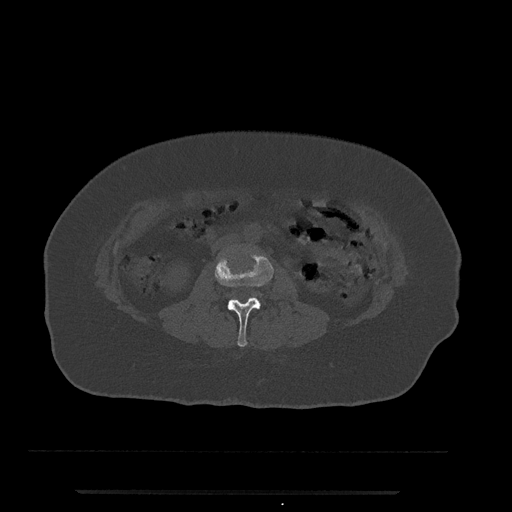
CT including the spine, one axial slice; position 16 of 797 along the scan axis; 120 kVp; bone window (W 1800 / L 400 HU); 0.5 mm slice thickness; 512 × 512 image matrix, field of view 440 × 440 mm. Female patient, age 51 years. Case-level facts recorded for this patient, not image findings: primary cancer: neuro; vertebrae with lytic lesions (as recorded): T8.
Outlined on this slice (semi-automatically segmented with operator editing):
- L2 vertebra: bounding box (x1, y1, x2, y2) in pixels: (214, 249, 274, 347)